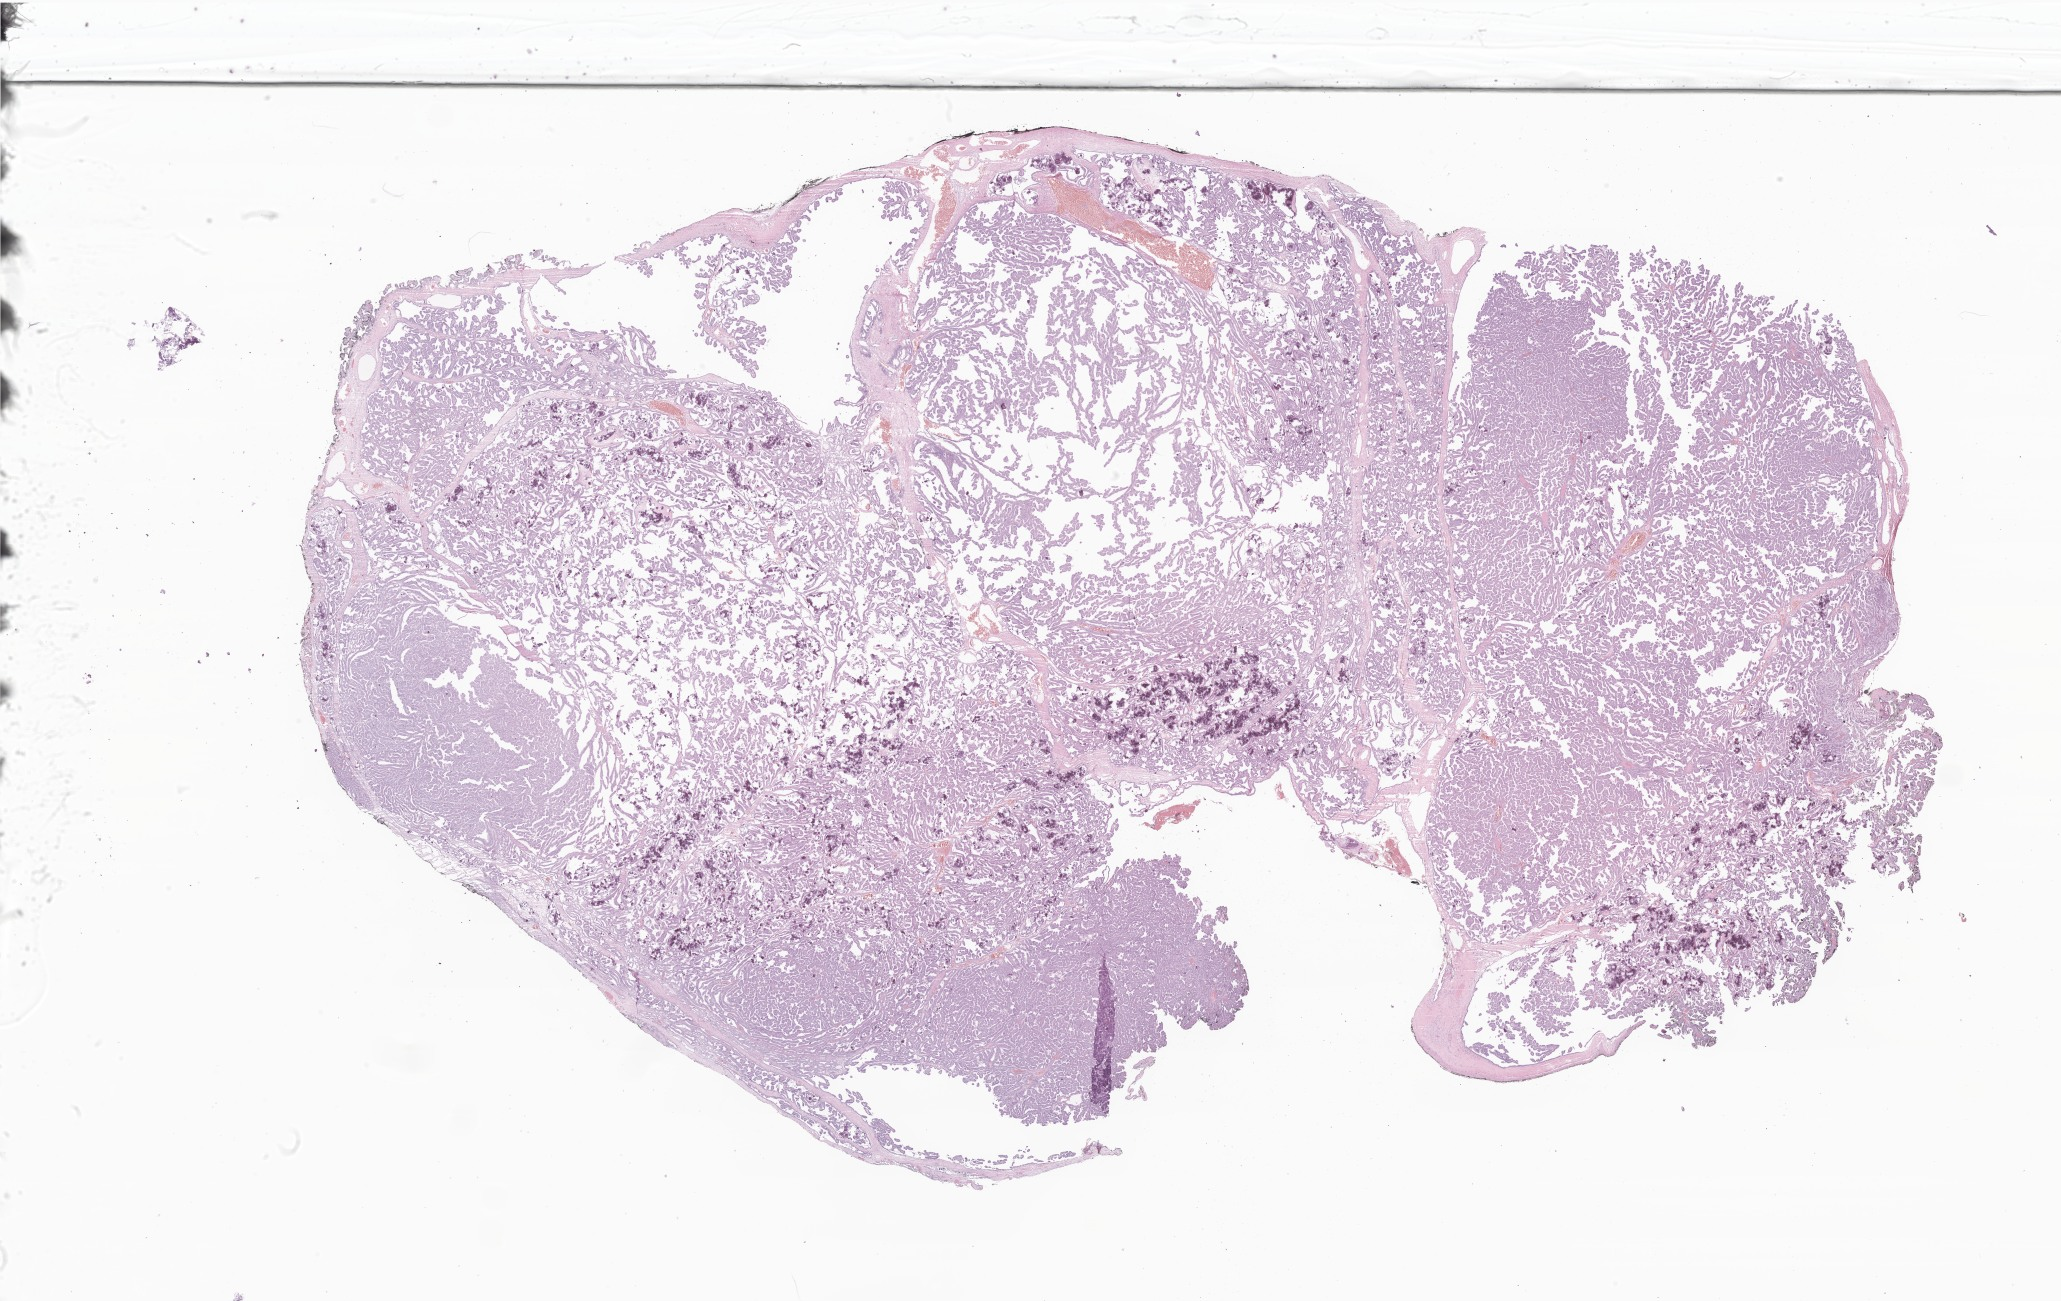
Digitized H&E-stained section of tumor tissue from the brain, shown as a low-resolution overview of the whole scanned area (about 34.8 x 21.9 mm), formalin-fixed, paraffin-embedded (FFPE) tissue. Patient female; age 38 months (3 years 2 months).
- recorded diagnosis: Choroid plexus papilloma, NOS